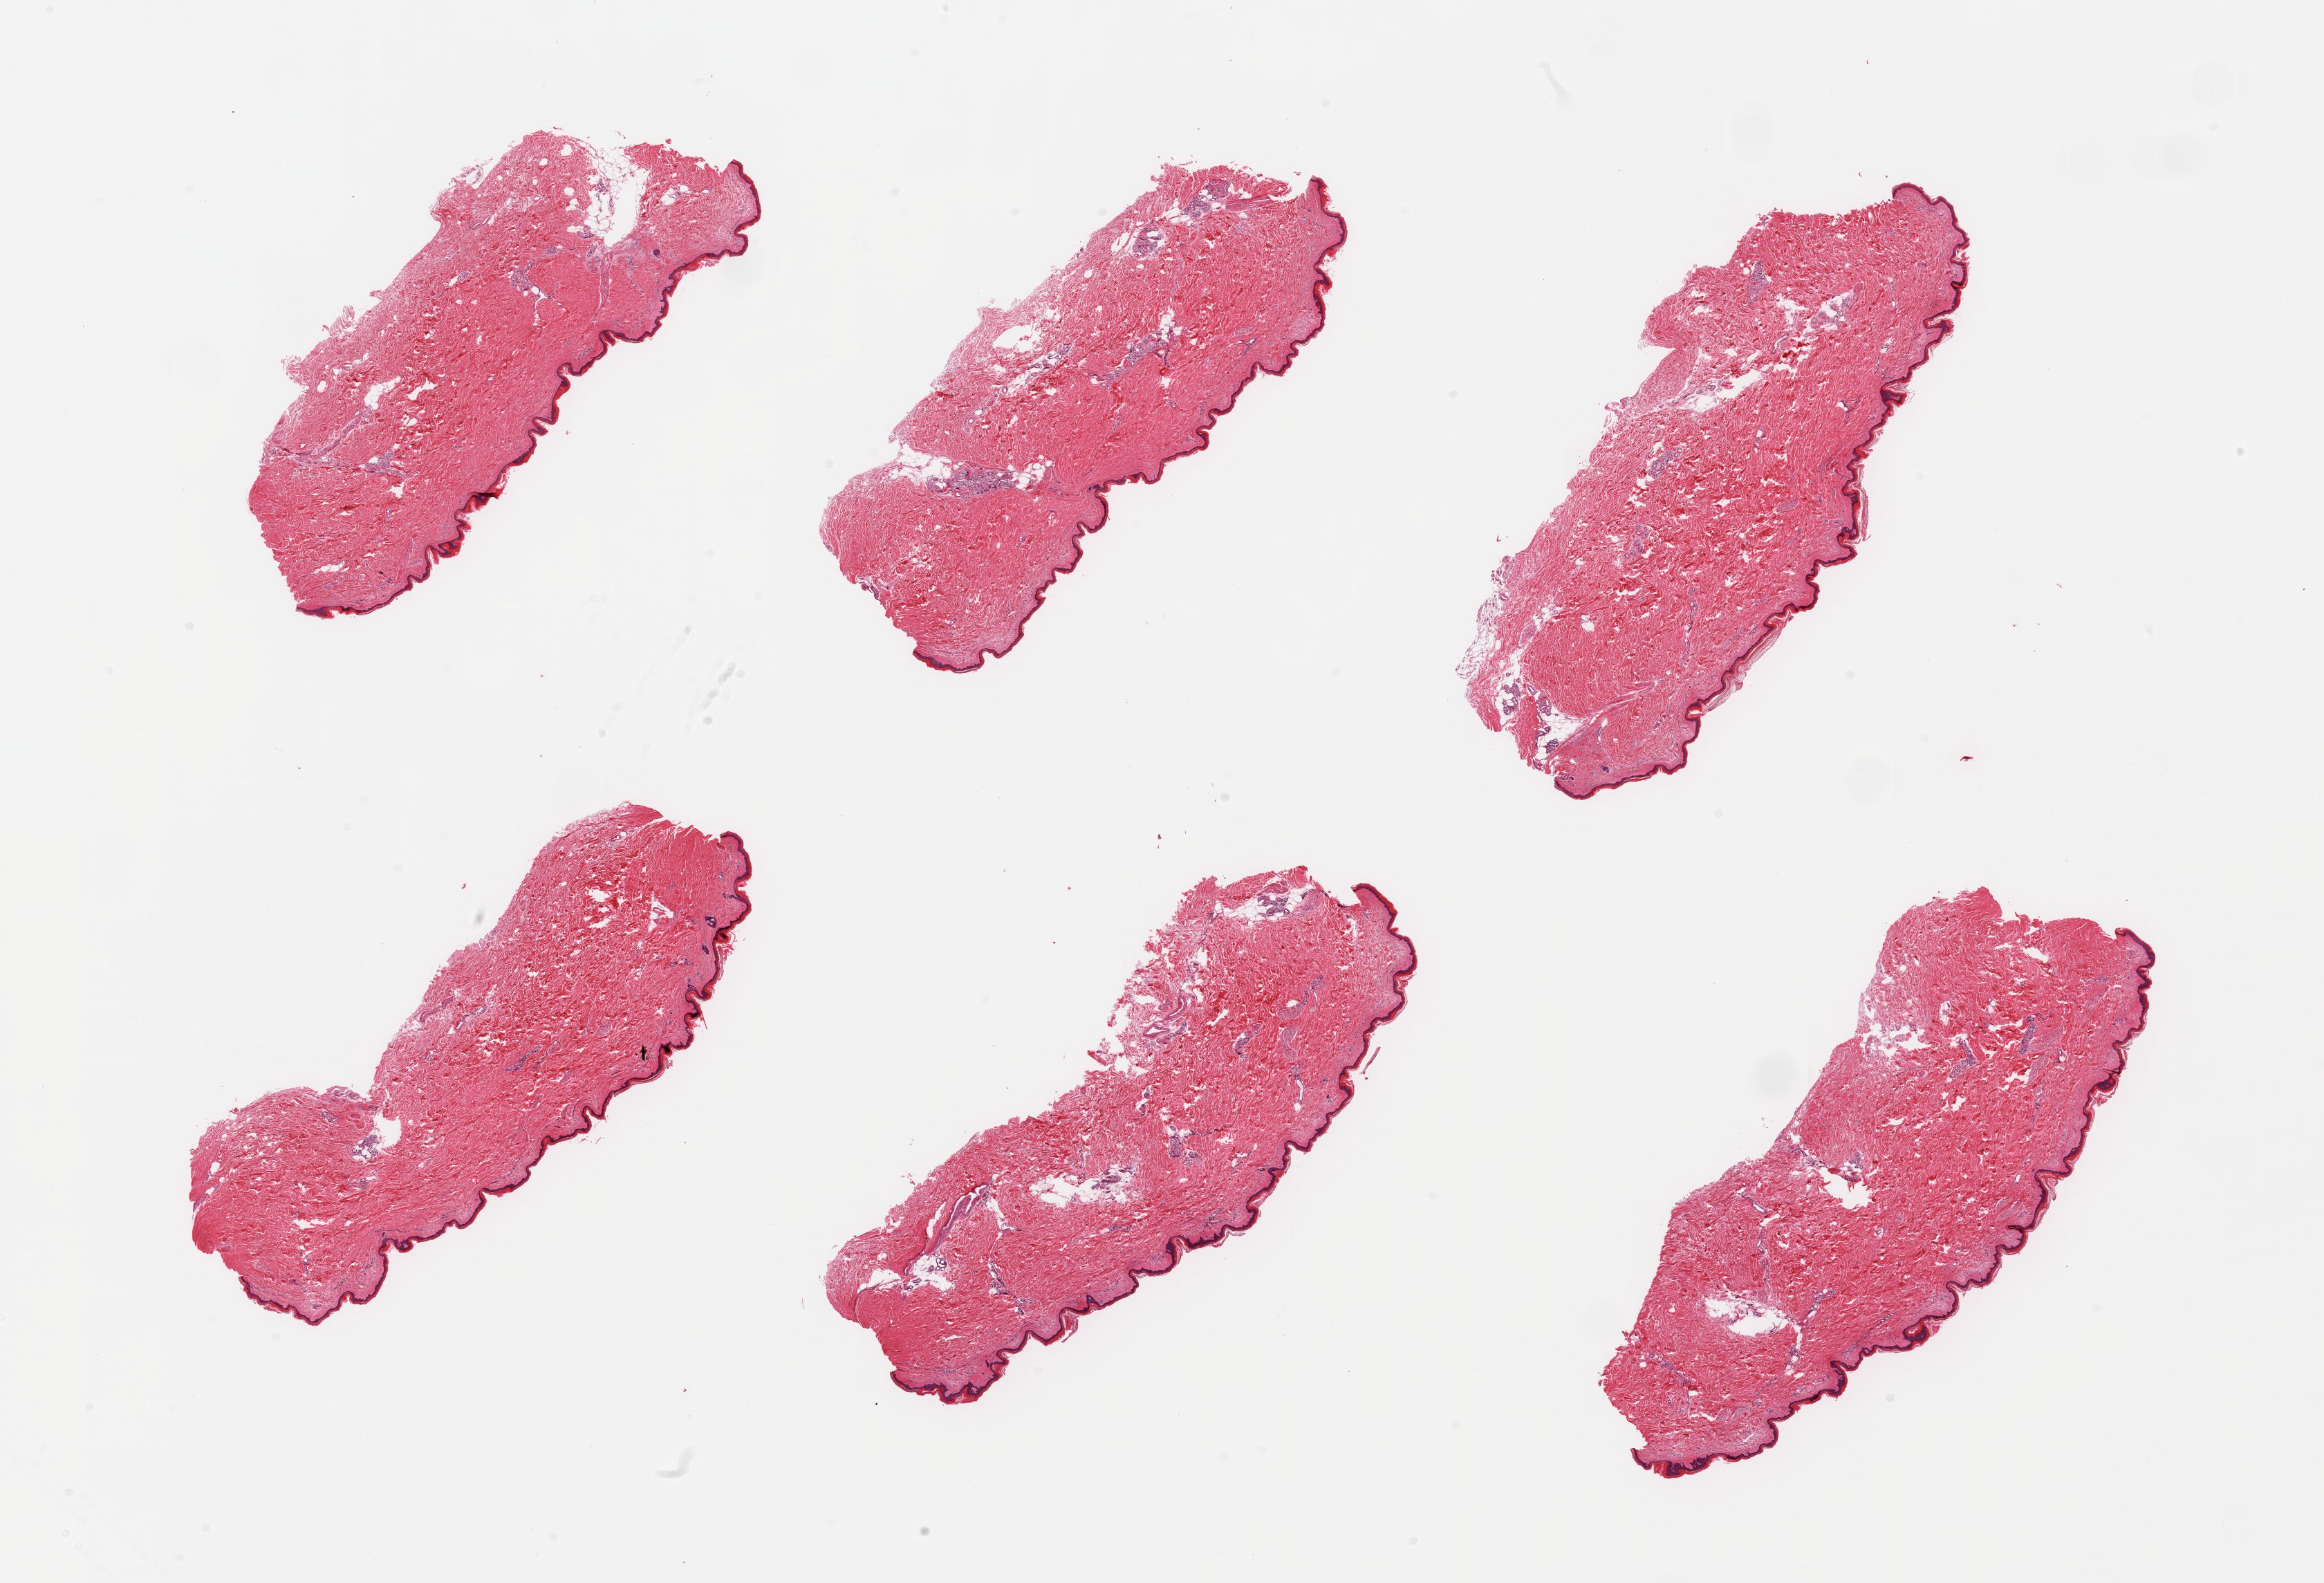
H&E whole-slide image — low-resolution overview of the scanned area, about 26.6 x 18.1 mm (from a 20x scan); PAXgene-fixed, paraffin-embedded tissue; sampled site (target tissue): skin of lower leg; tissue donor sample. Male donor.
Pathologist's review note for this sample: 6 pieces, trace dermal fat; squamous epithelium is ~40 microns.